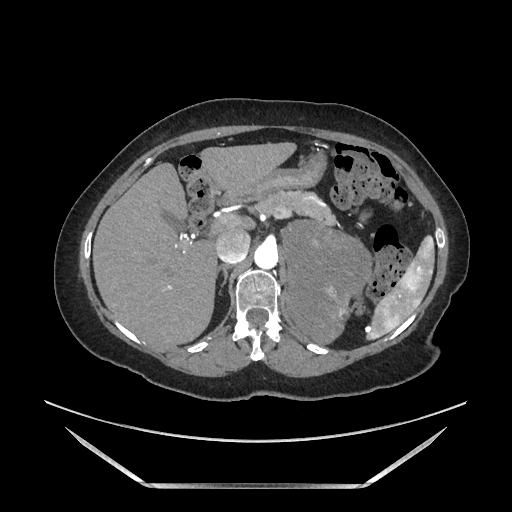
Contrast-enhanced abdominal CT, one axial slice. Soft-tissue window (W 400 / L 40 HU). 1.25 mm slice thickness. 512 × 512 image matrix, field of view 440 × 440 mm. Female patient. From the clinical record (not read from this slice): diagnosis: adrenocortical carcinoma; tumour side: left adrenal; tumour size at pathology: 12.5 cm; Ki-67 index: 39 %; stage (as recorded): 3.
Structures marked on this image (semi-automatically segmented with operator editing):
- mass: bounding box (x1, y1, x2, y2) in pixels: (286, 223, 370, 345)